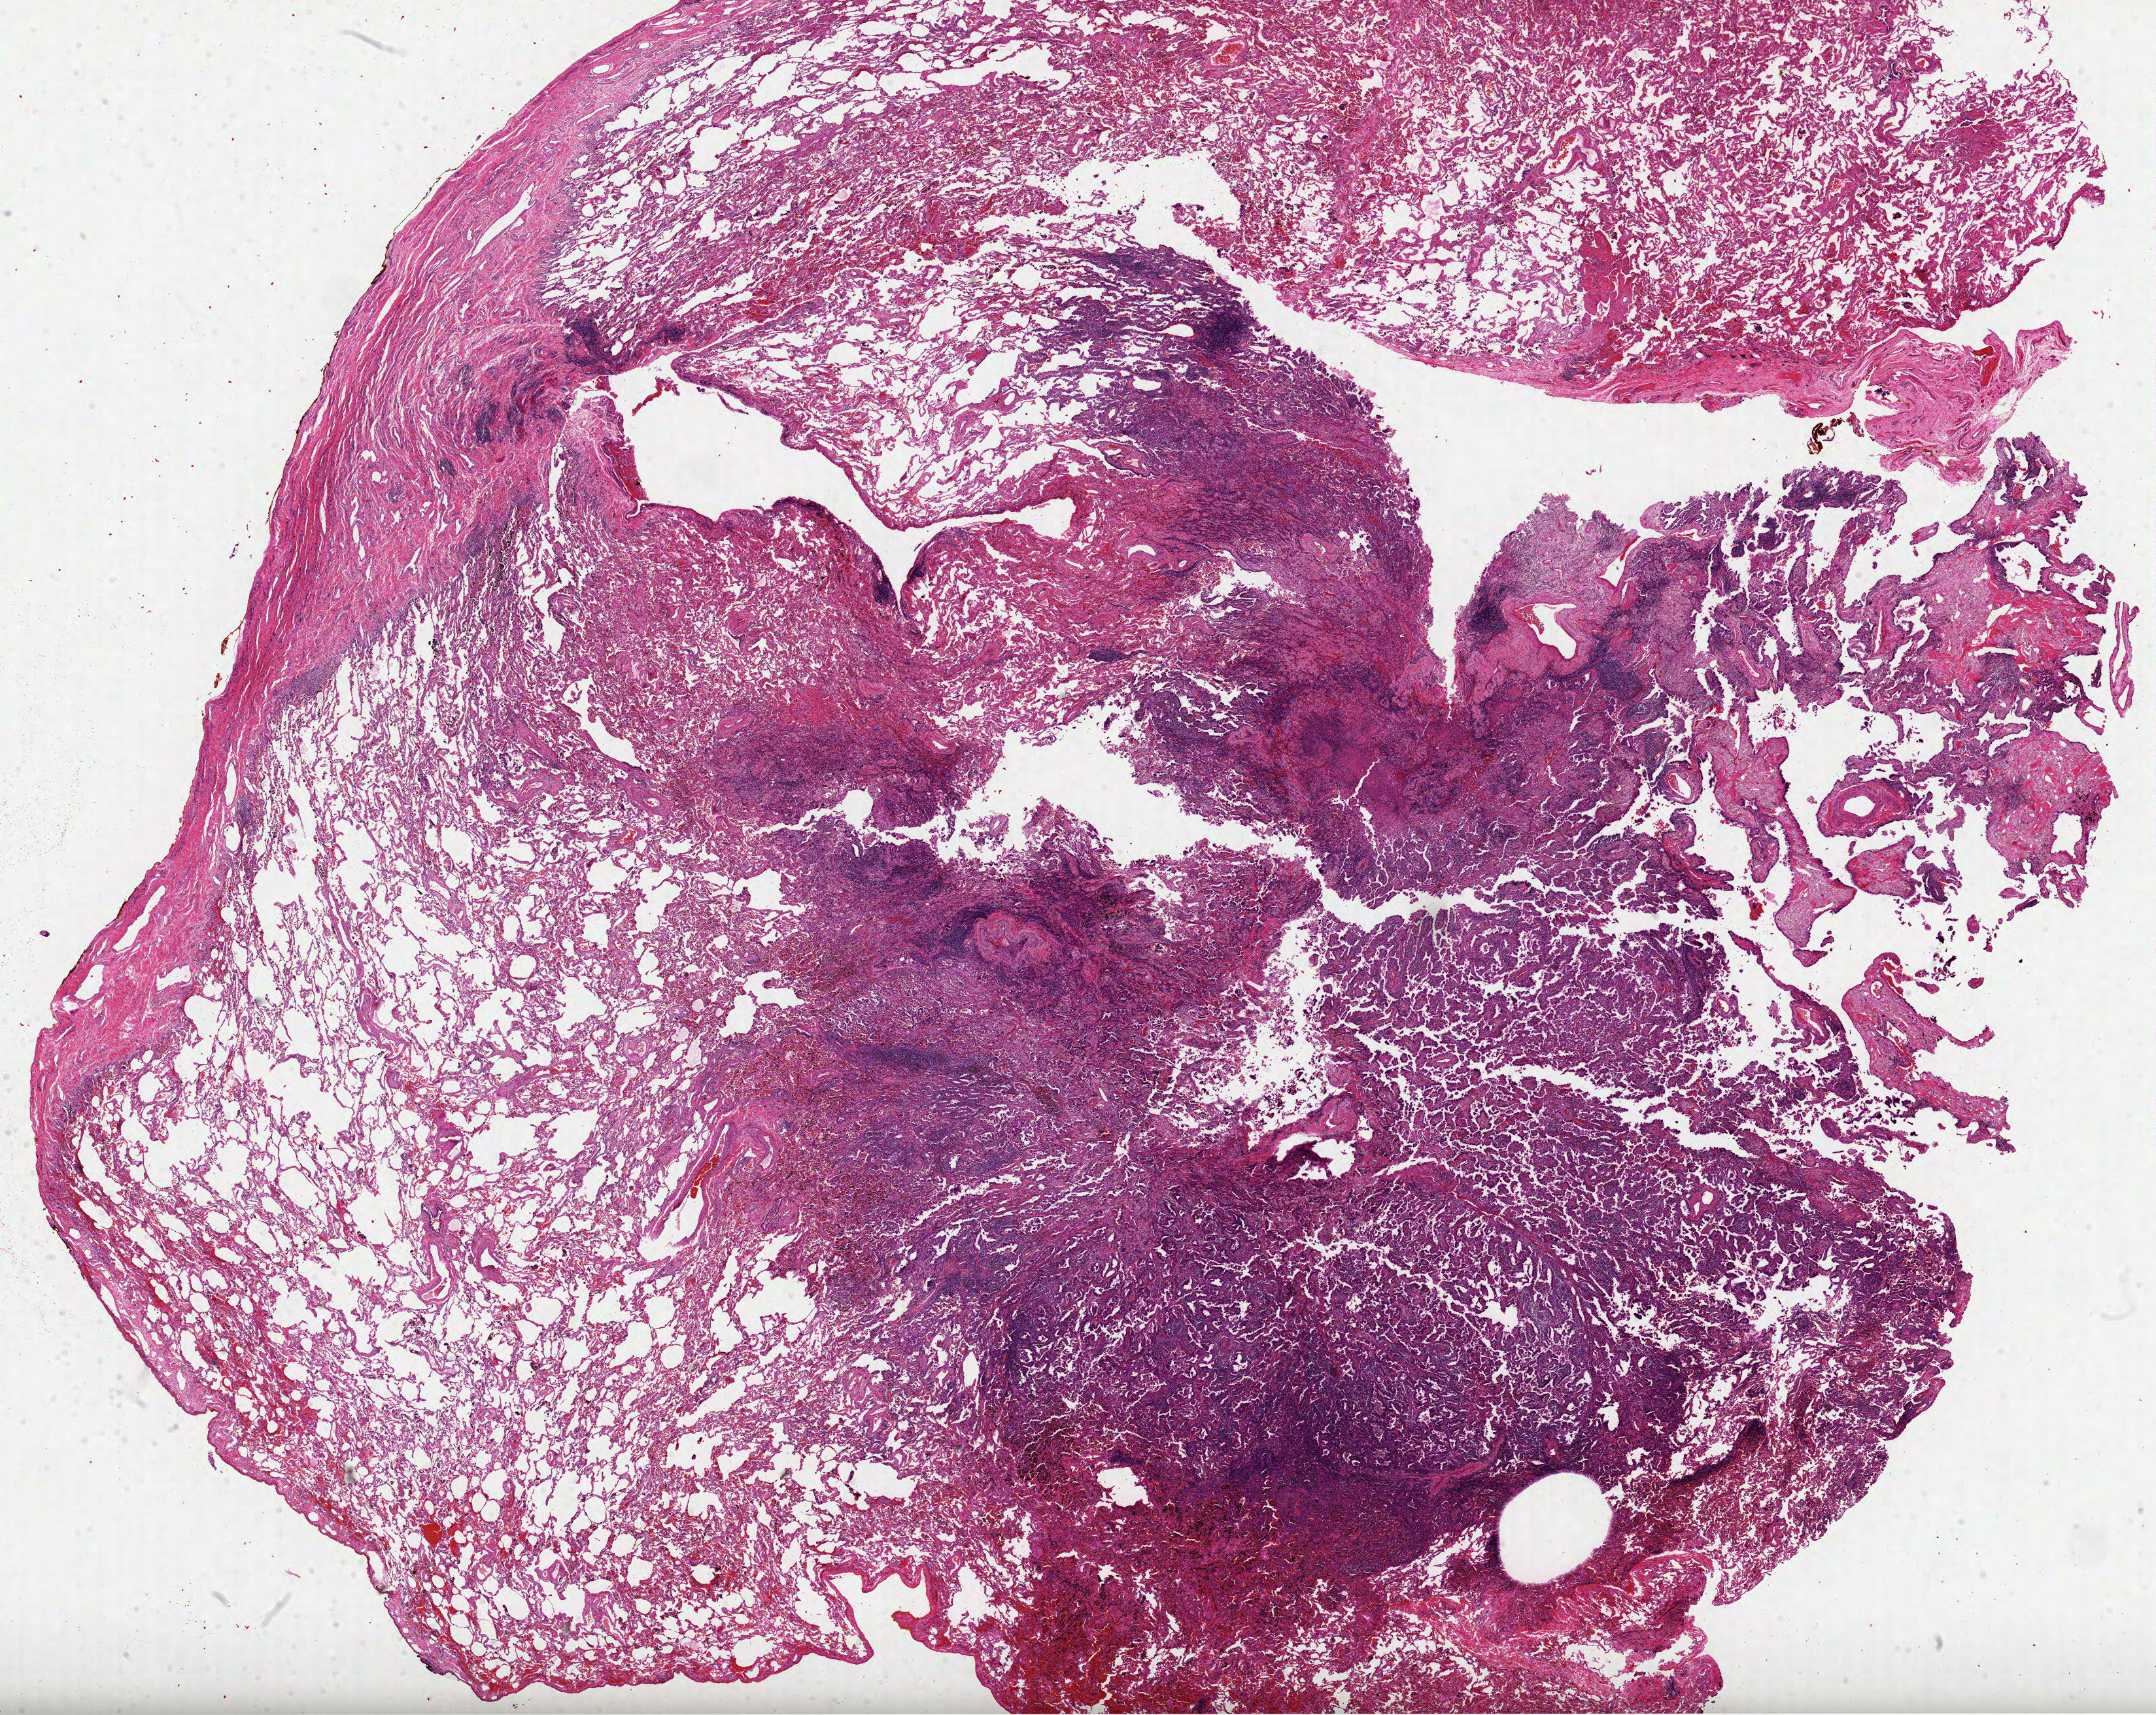
H&E whole-slide image, a low-resolution overview of the entire scanned area, about 26.6 x 21.2 mm; FFPE section; lung, primary tumour sample. Female, age 64 years at initial diagnosis.
AJCC pathologic stage: IIA (7th edition). Diagnosis: Adenocarcinoma with mixed subtypes (upper lobe, lung).